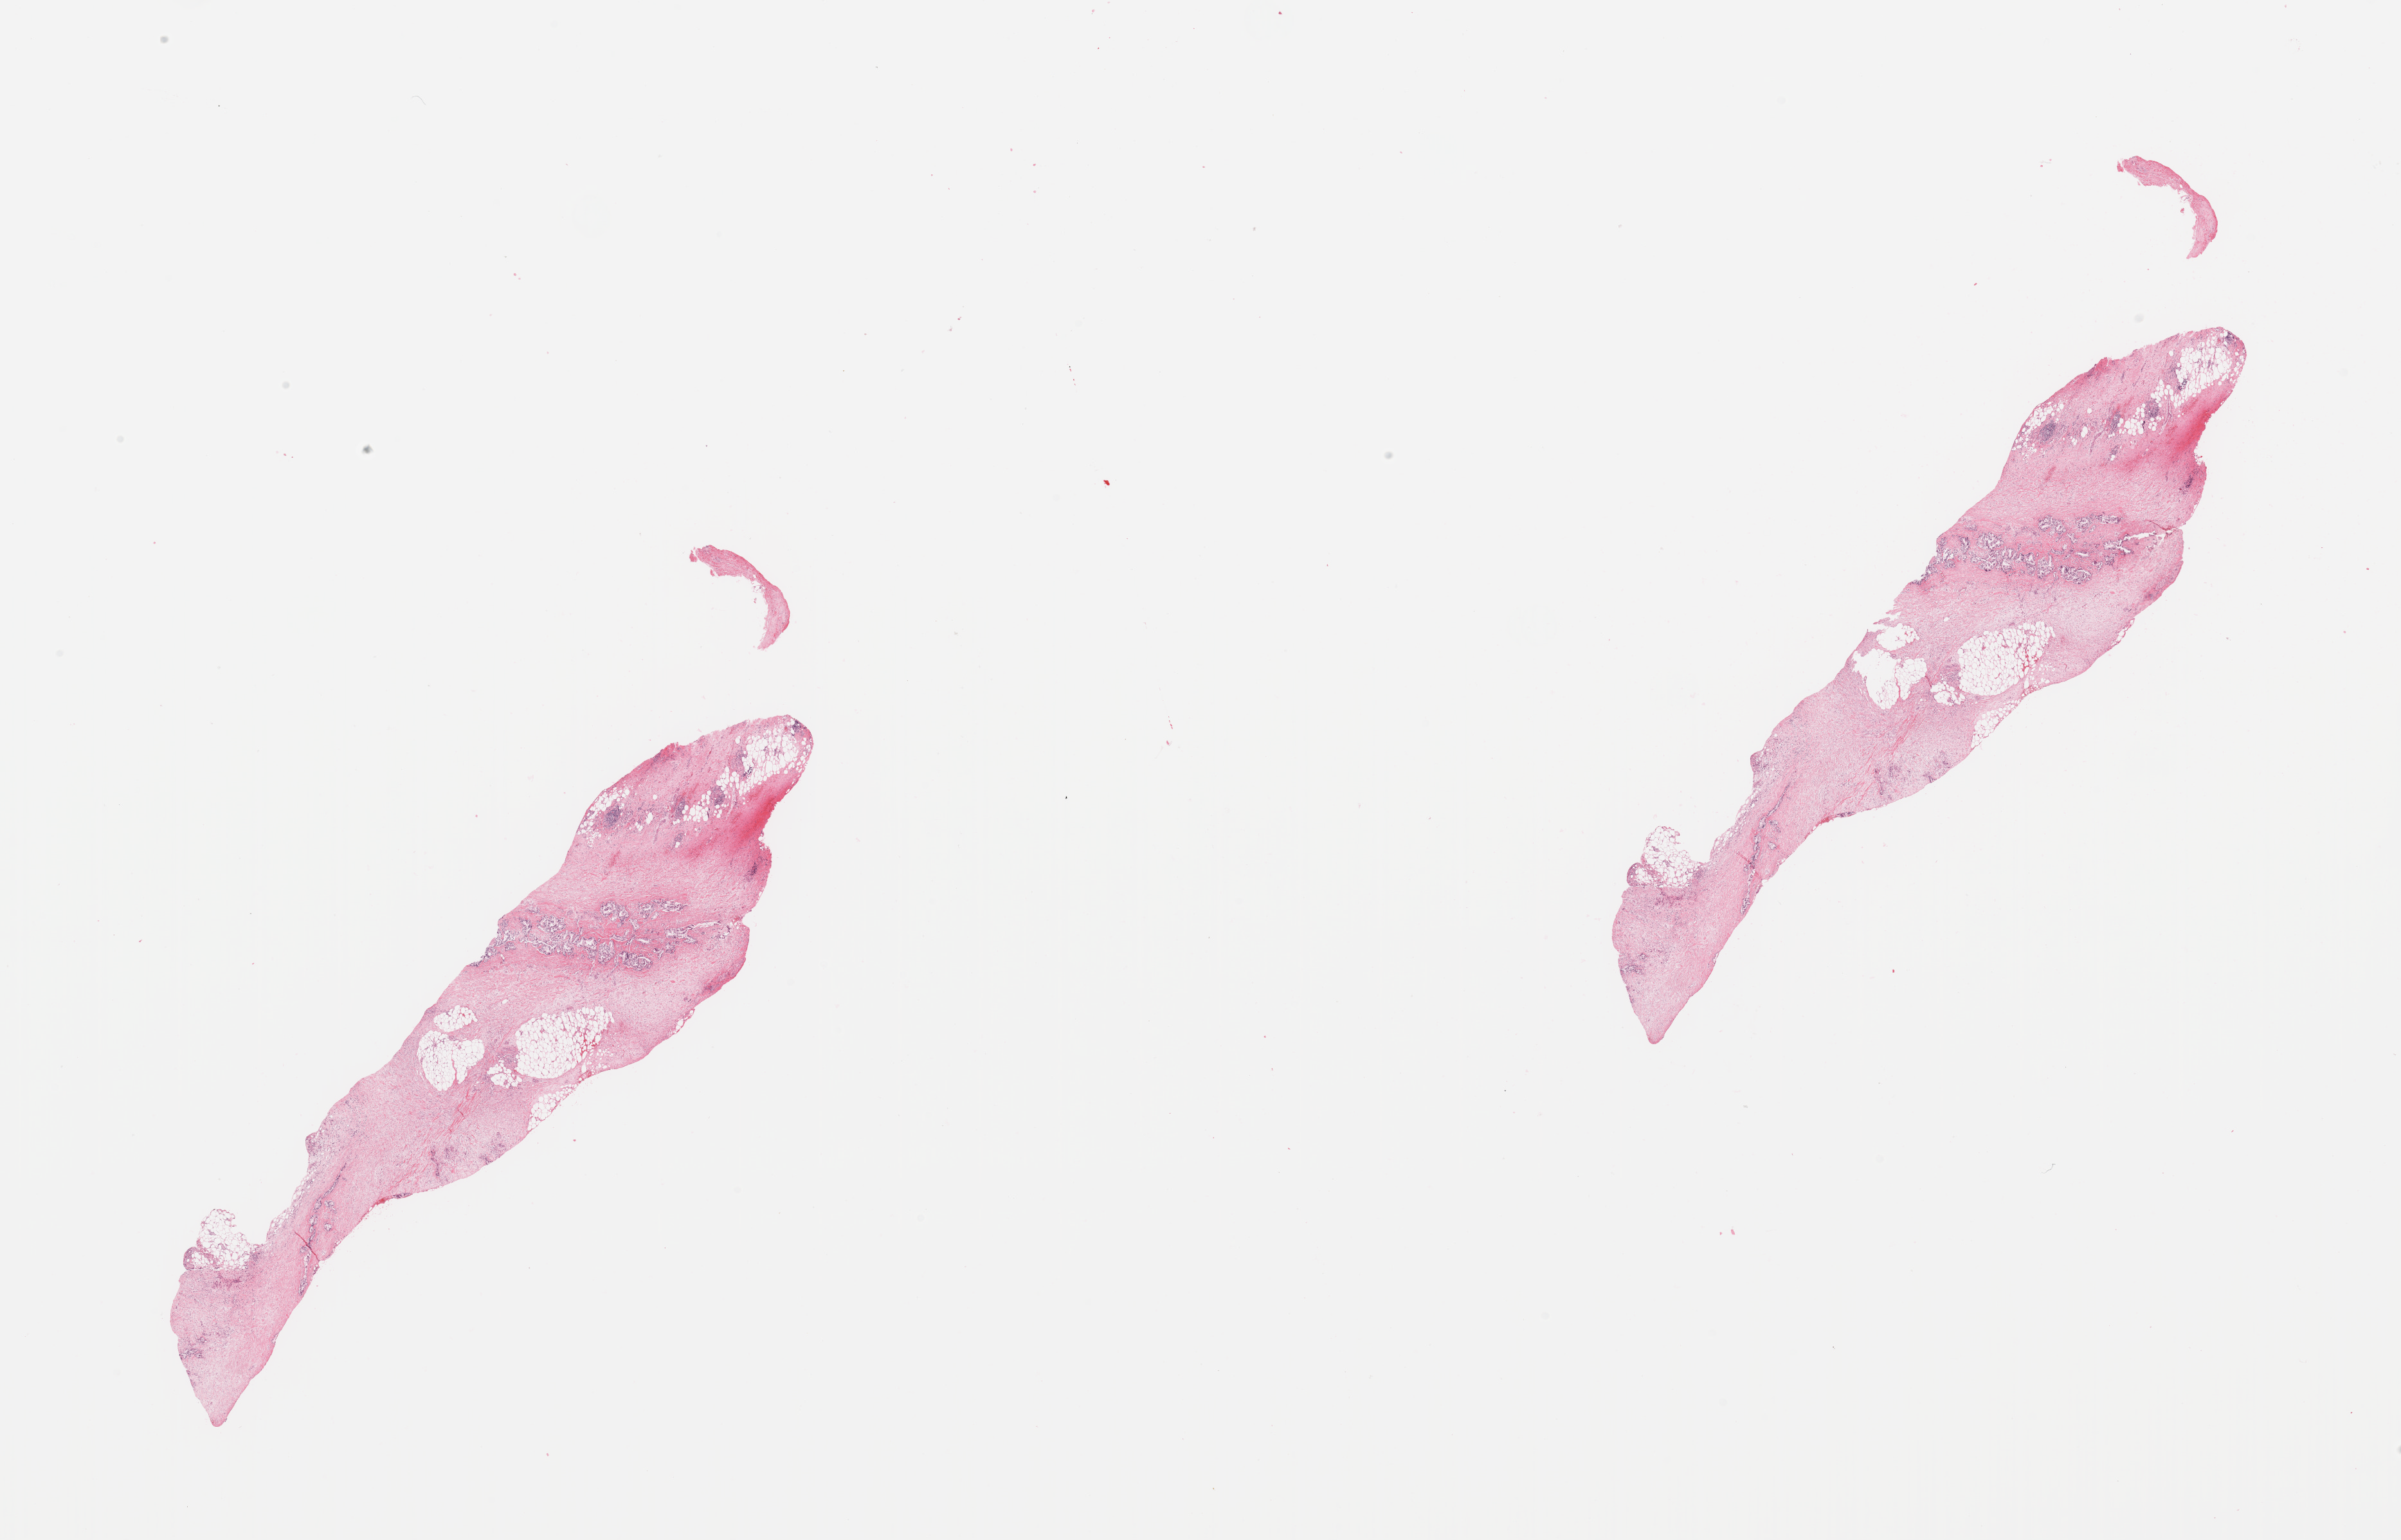
Whole-slide histology image, Hematoxylin and eosin (H&E) stained, whole scanned area (about 29.5 x 18.9 mm) shown as a low-resolution overview. Pancreas, tumour tissue. Patient: female, age 78 years. Histologic grade: G1 (well differentiated).
• histologic diagnosis: Infiltrating duct carcinoma, NOS
• AJCC pathologic stage: III
• primary tumour site (as recorded): tail